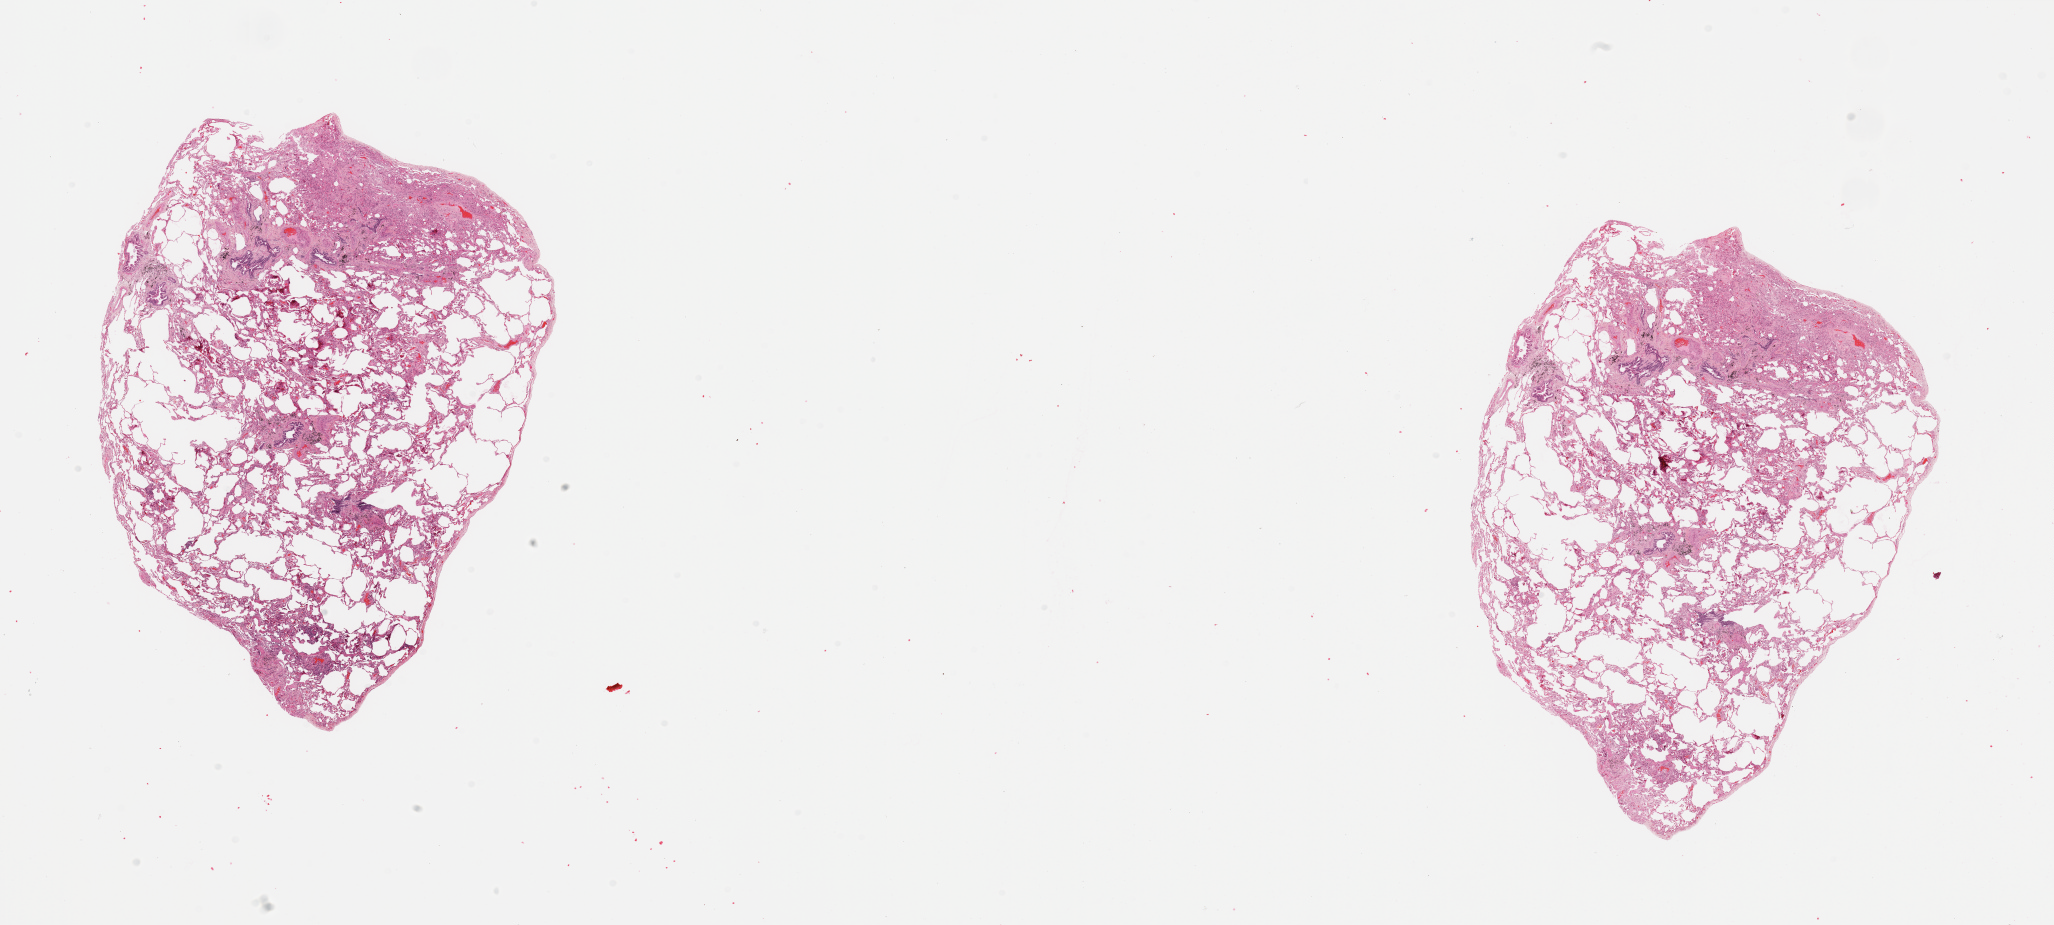
H&E whole-slide image, whole scanned area (about 32.5 x 14.6 mm) shown as a low-resolution overview; normal (non-tumour) tissue sample, sampled site: lung. Patient: female, age 69 years.
This section: normal (non-tumour) tissue from the same patient. Patient diagnosis: Adenocarcinoma, NOS.